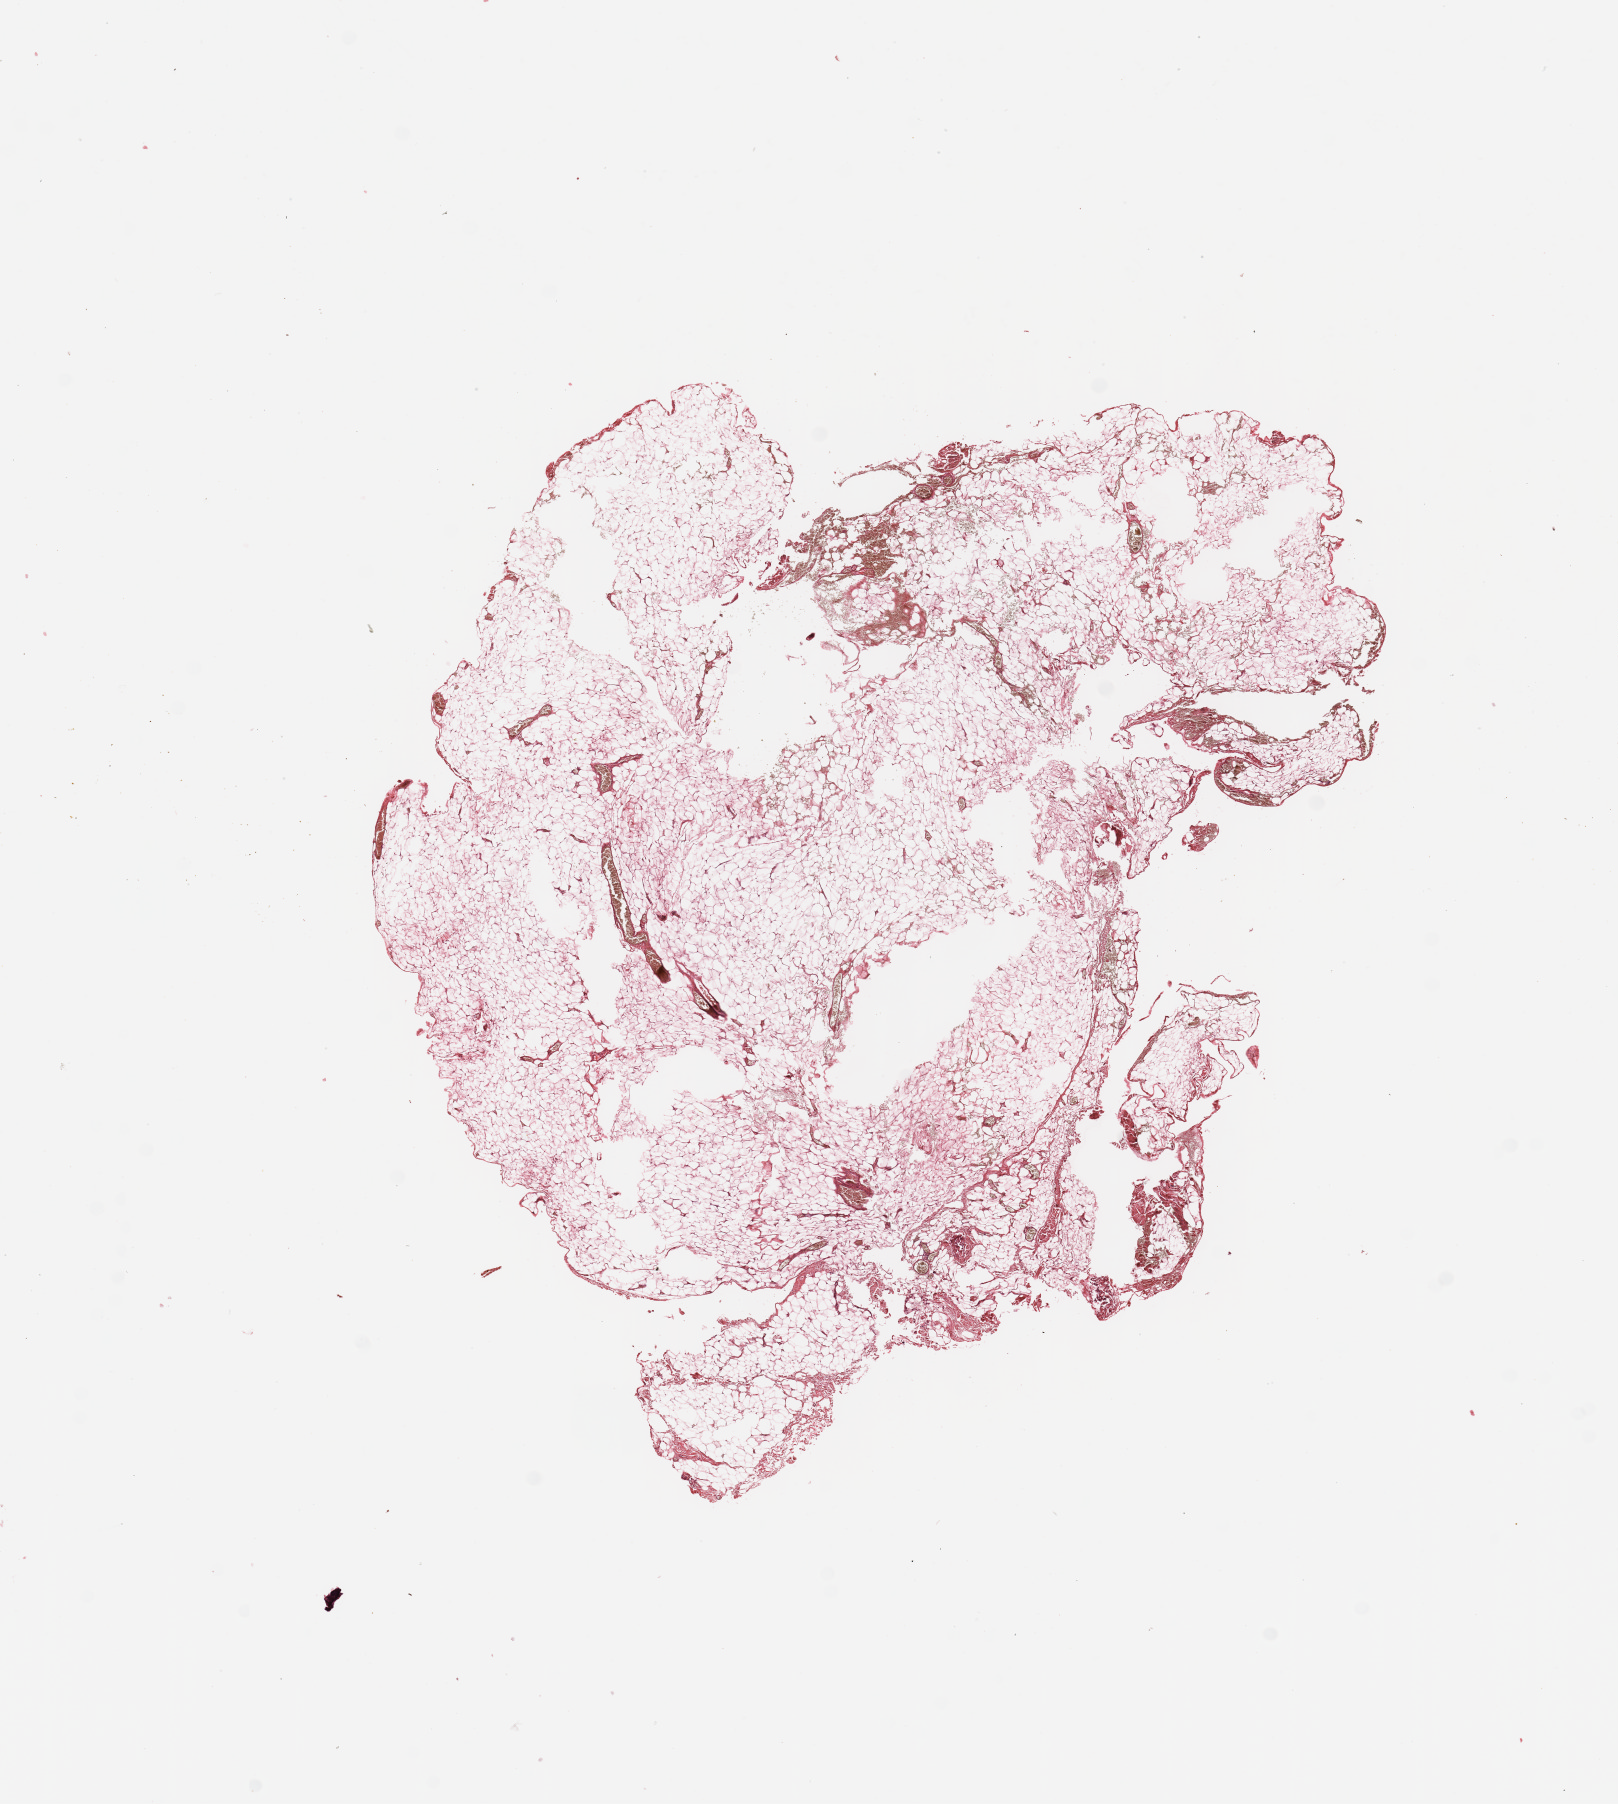
Digitized H&E-stained tissue section (whole slide) — shown as a low-resolution overview of the whole scanned area (about 12.8 x 14.3 mm, acquisition: 20x scan), normal (non-tumour) tissue sample, sampled site: lymph node. 63-year-old female patient.
This section: normal (non-tumour) tissue from the same patient. Patient diagnosis: Malignant melanoma, NOS.